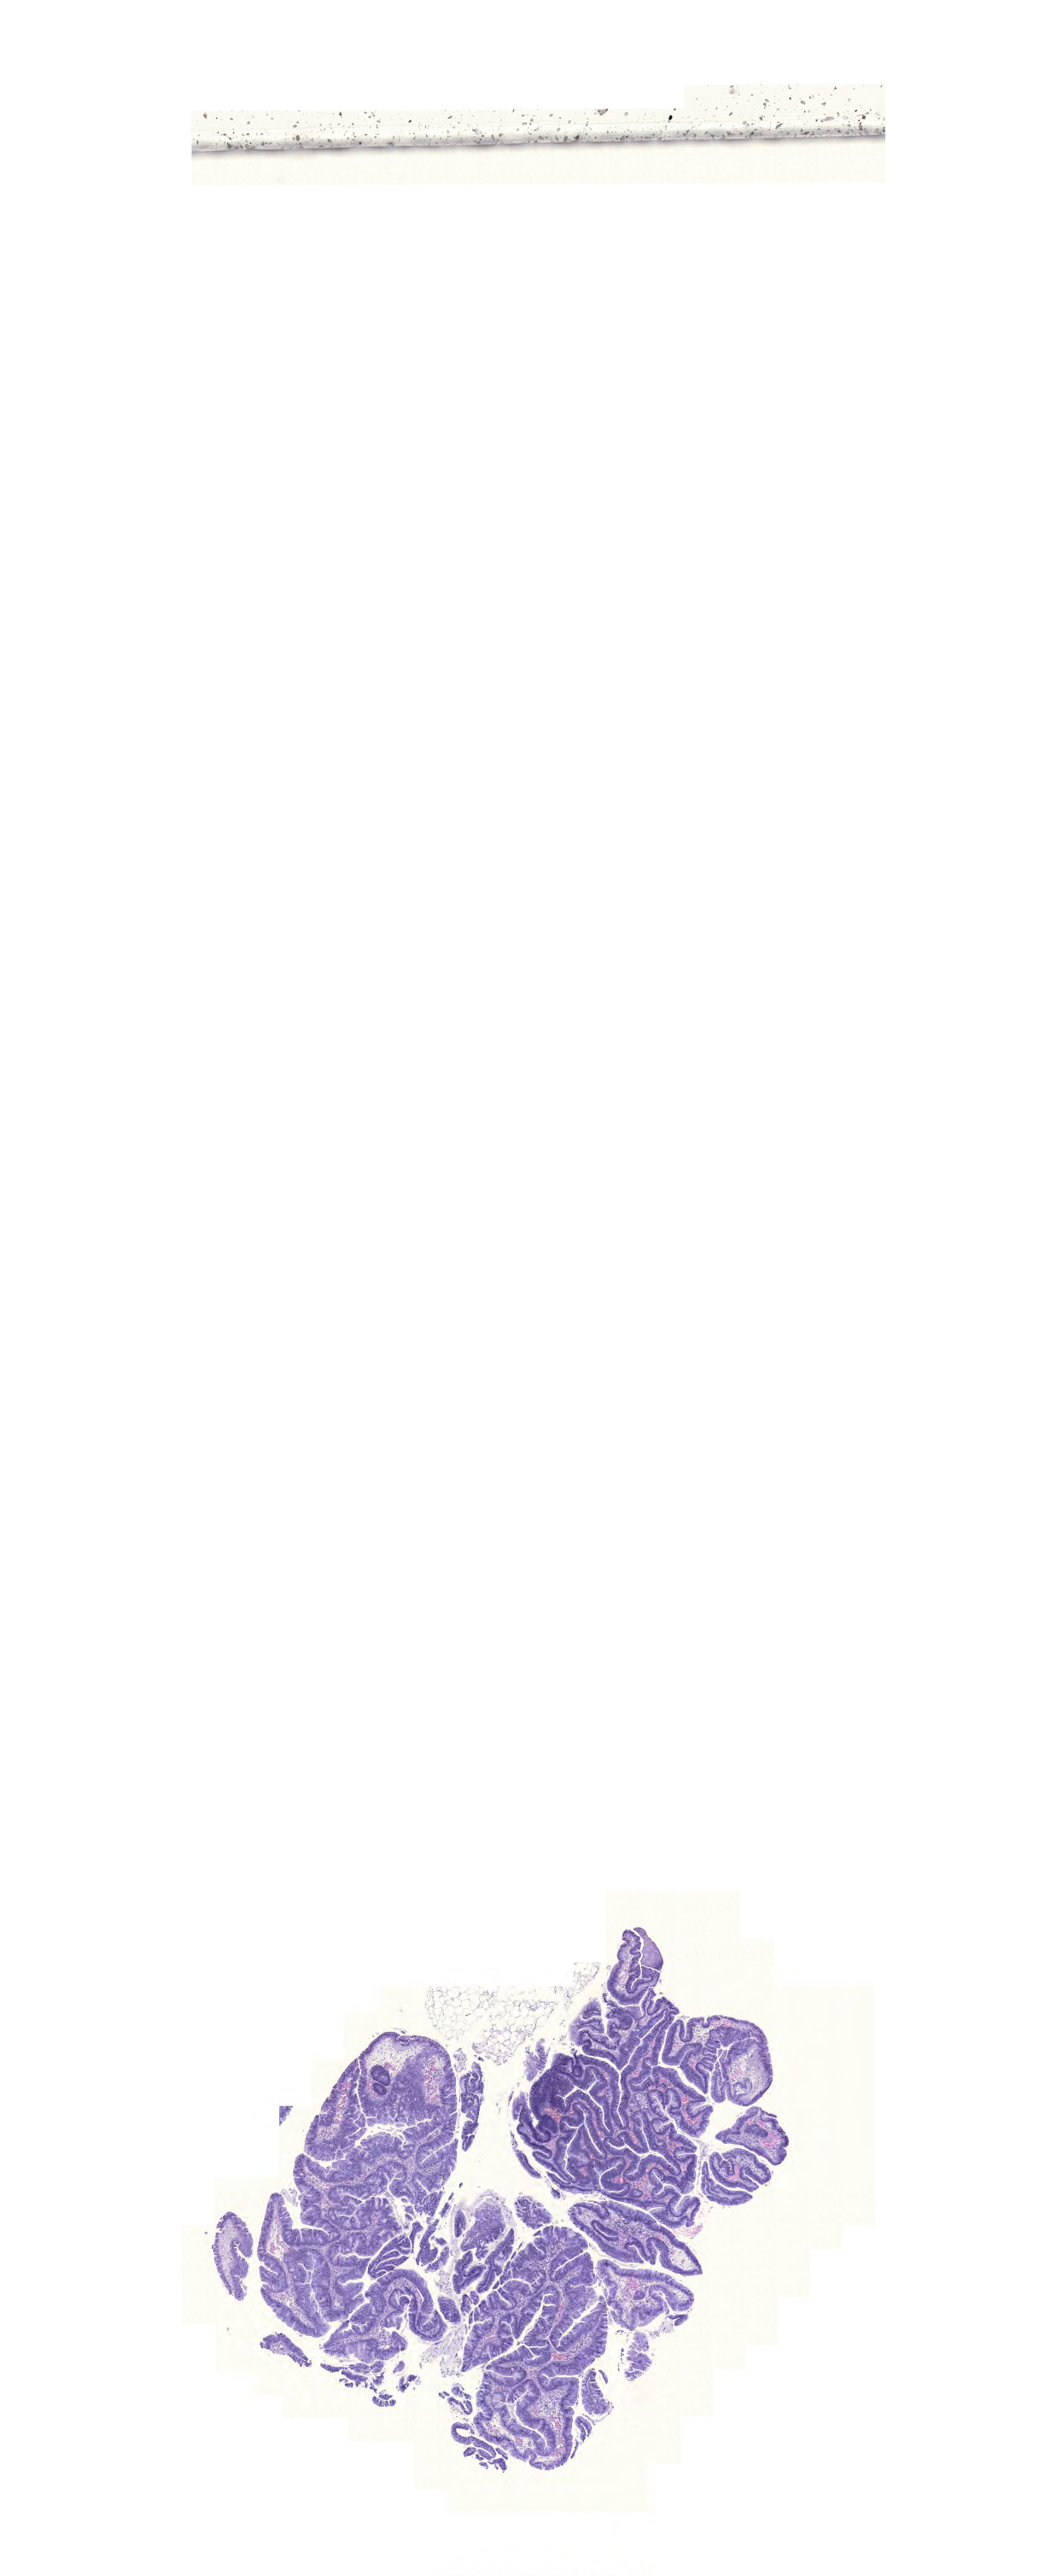
Whole-slide histology image, H&E — low-resolution overview of the scanned area, about 9.1 x 22.4 mm, FFPE section, sample: primary tumour, colon. Female patient; age at initial diagnosis 71 years.
Lymph nodes positive (case pathology): 0 of 12 examined. AJCC pathologic stage: I (6th edition). Diagnosis: Mucinous adenocarcinoma.